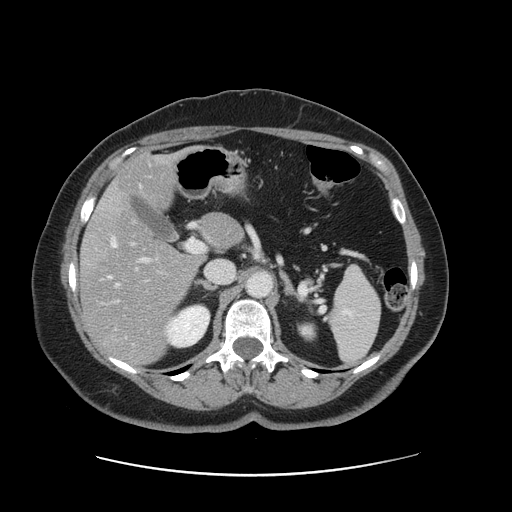
Contrast-enhanced abdominal CT, one axial slice. Position 83 of 161 along the scan axis. Intravenous contrast given. Soft-tissue window (W 400 / L 40 HU). 512 × 512 image matrix. Female patient, age 62 years. From the clinical record (not read from this slice): diagnosis: colorectal cancer liver metastases, imaged before liver resection.
Outlined on this slice (manually delineated by an expert):
- hepatic veins: box from (x=108, y=185) to (x=142, y=287) px
- liver: (x=81, y=156)–(x=240, y=364)
- planned liver remnant (the part of the liver to remain after resection): (x=111, y=156)–(x=240, y=247)
- portal vein (with intrahepatic branches): (x=110, y=240)–(x=204, y=303)